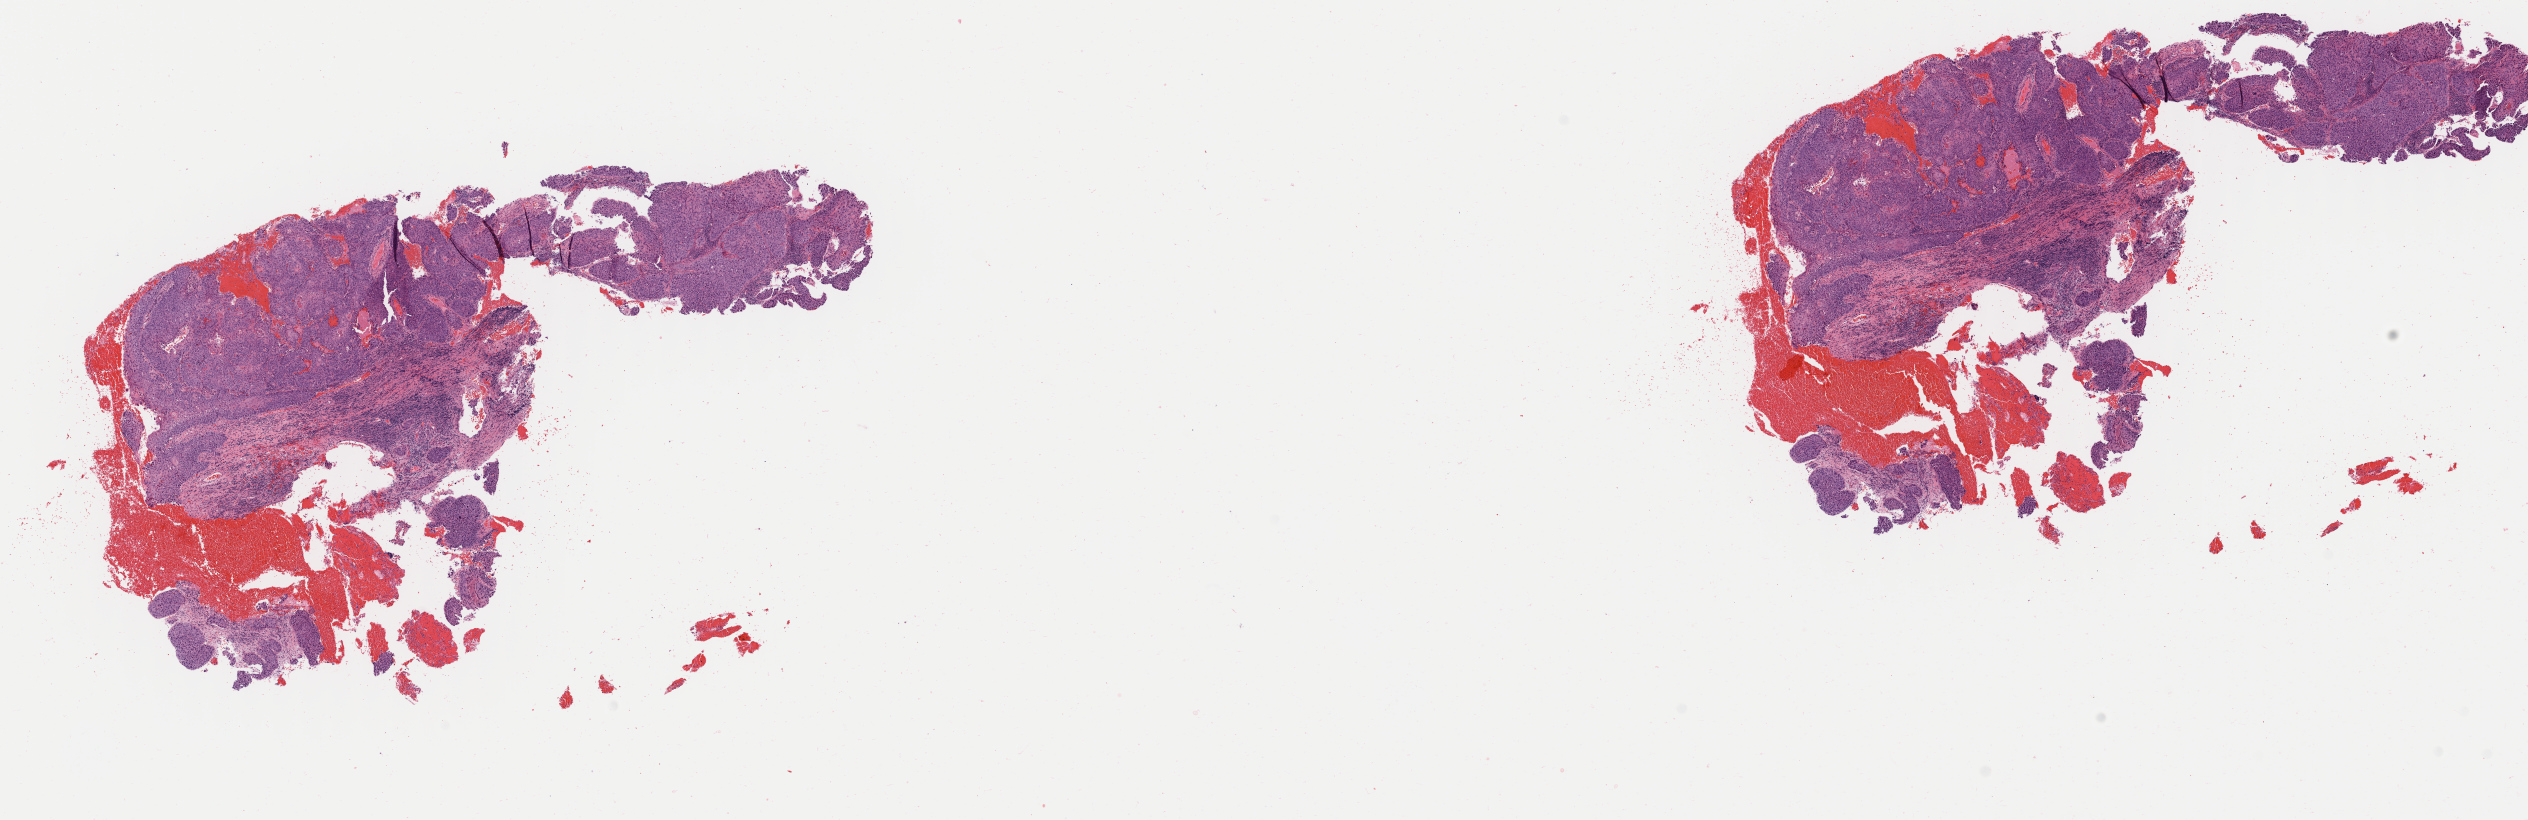
Hematoxylin and eosin (H&E) whole-slide image — shown as a low-resolution overview of the whole scanned area (about 20.1 x 6.5 mm), tumor tissue, anatomic site: cervix. Female patient, aged 65.
- diagnosis: Squamous cell carcinoma, keratinizing, NOS